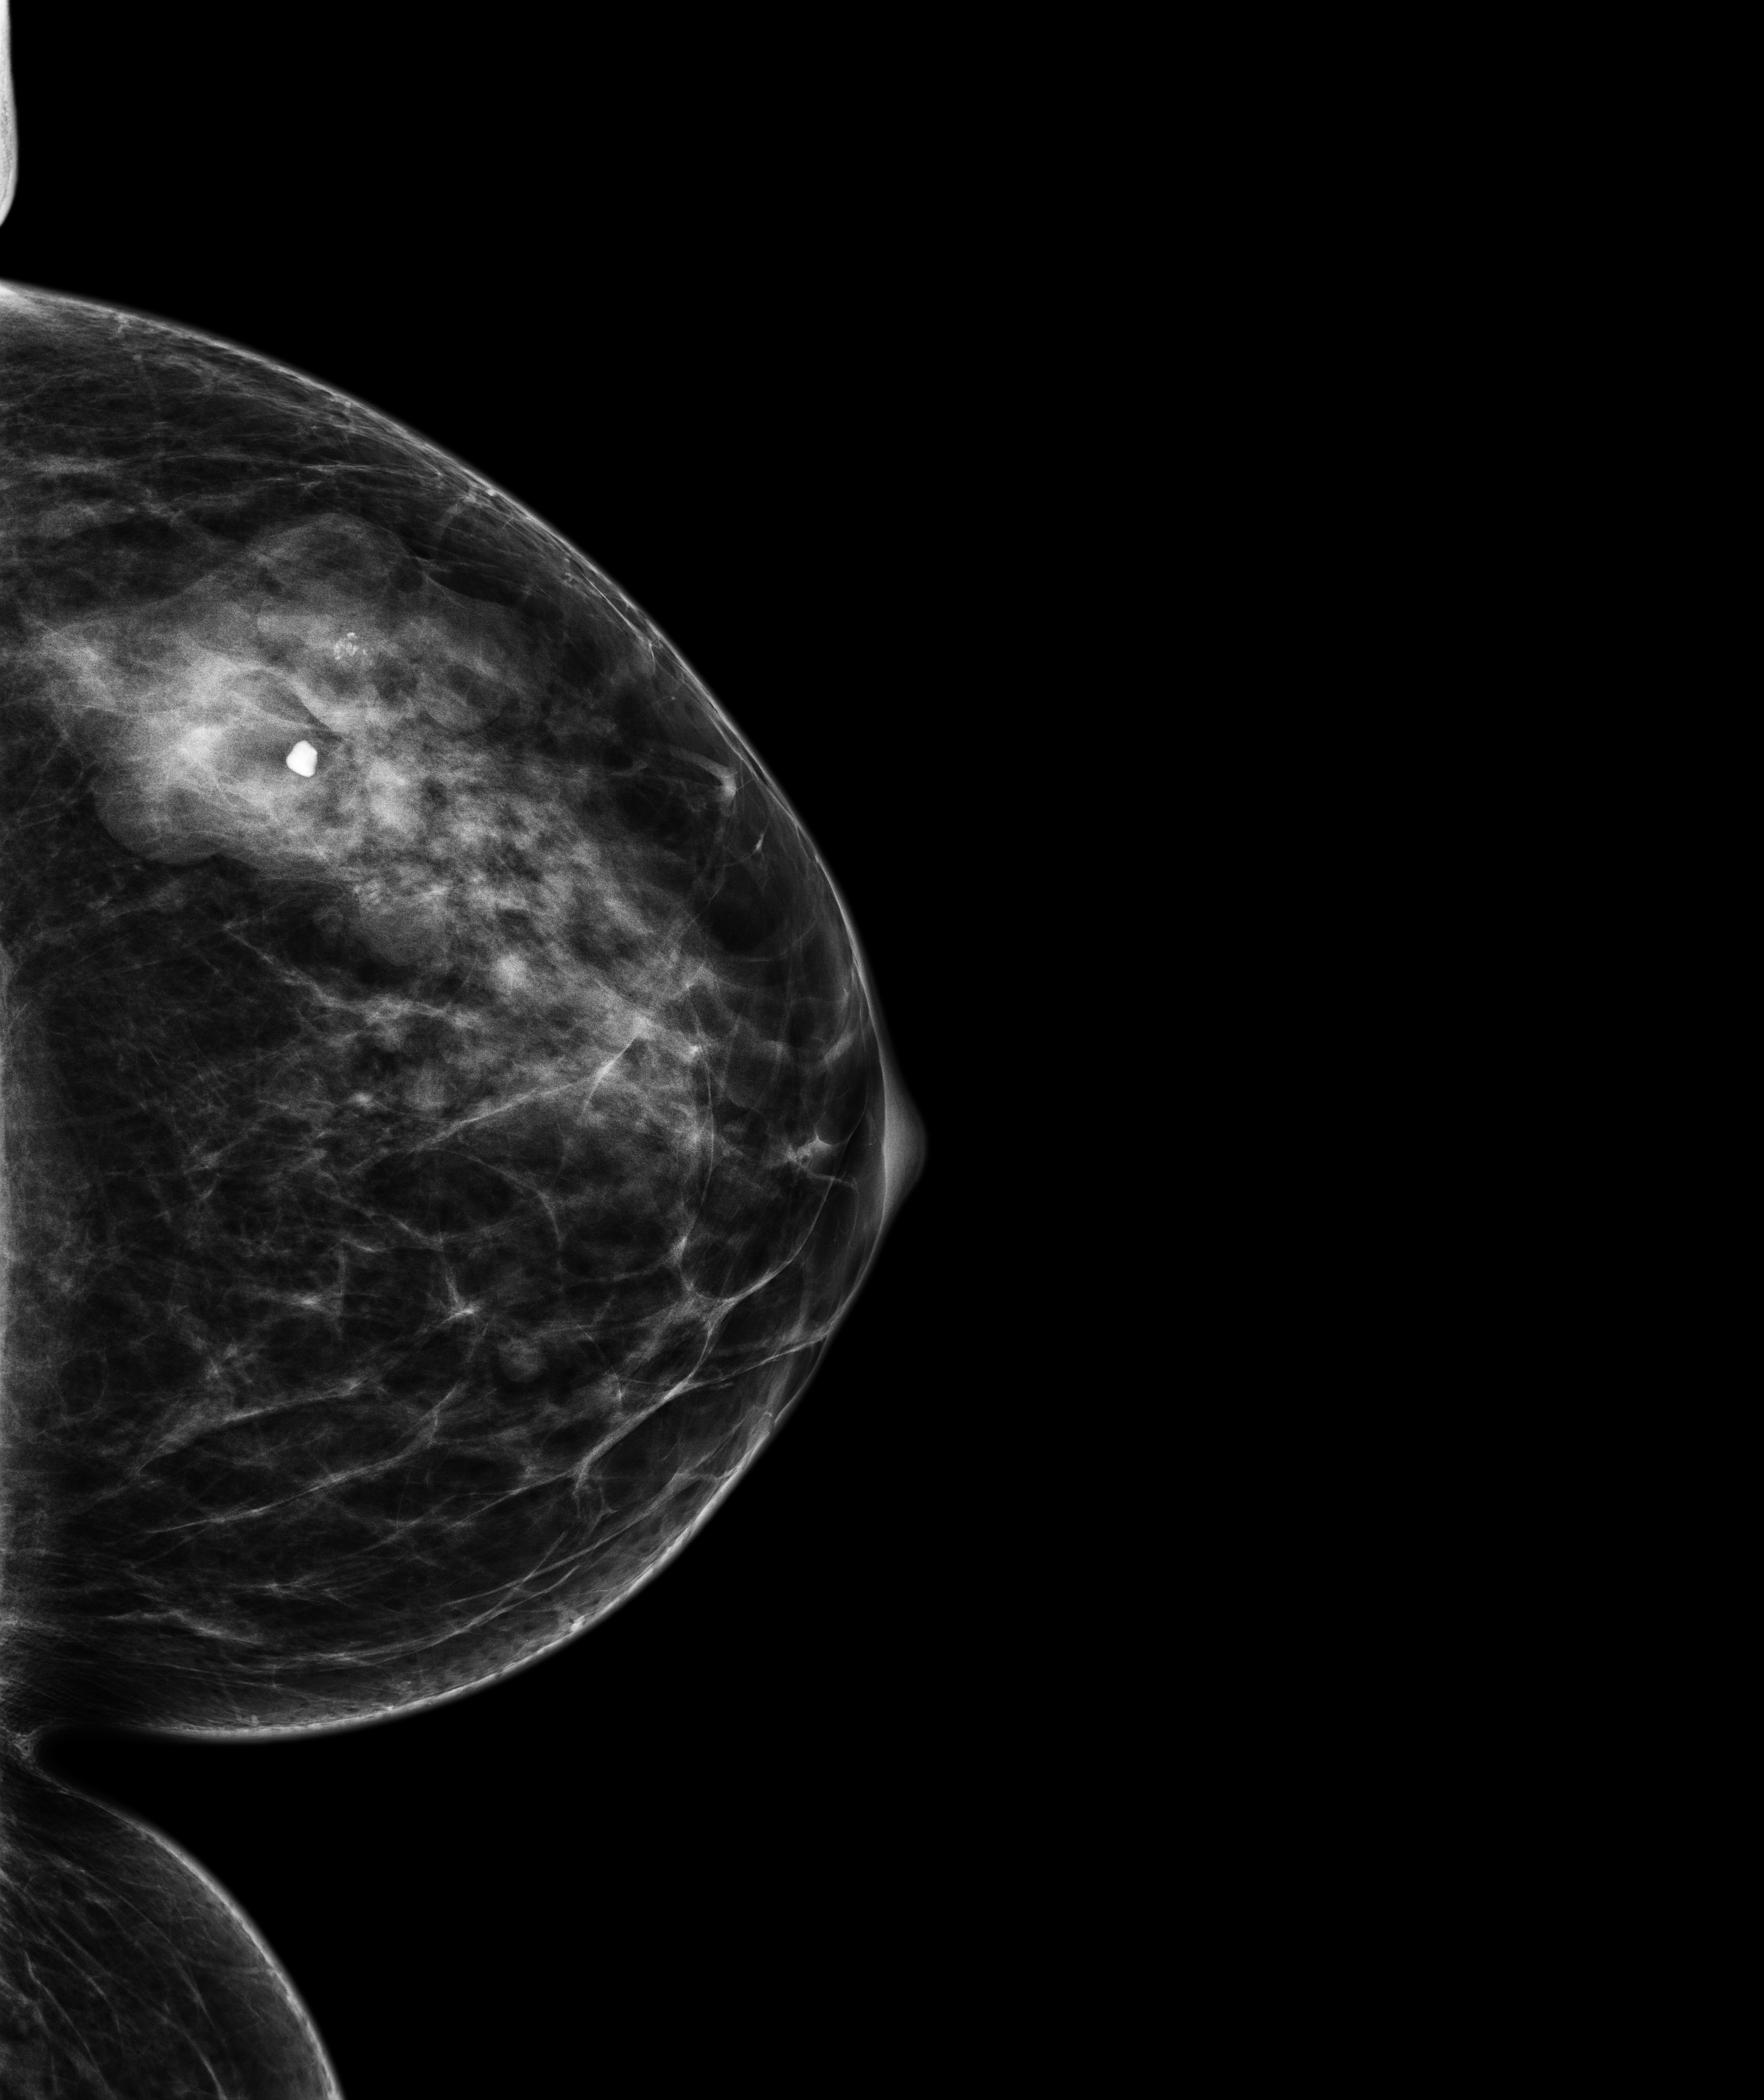
Screening examination. Patient aged 52 years (female).
Image type: full-field digital mammogram. Breast: left. Projection: craniocaudal (CC) view.